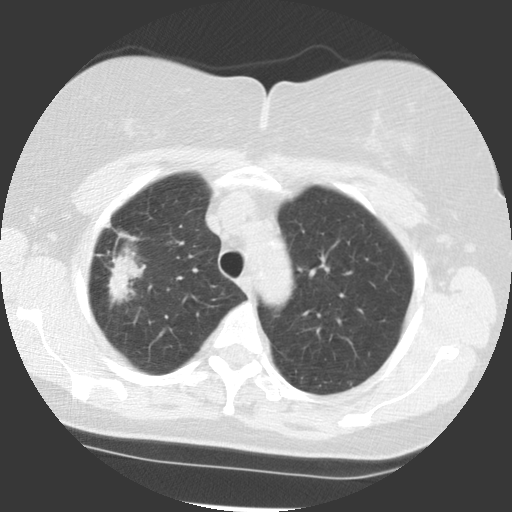
Low-dose screening chest CT, one axial slice; reconstruction kernel STANDARD; 140 kVp; lung window (W 1500 / L -600 HU); 2.5 mm slice thickness; 512 × 512 image matrix.
Outlined on this slice (outlined manually by an expert reader):
- lesion 1 (tumor, upper lobe of right lung): bounding box (x1, y1, x2, y2) in pixels: (108, 246, 146, 304)